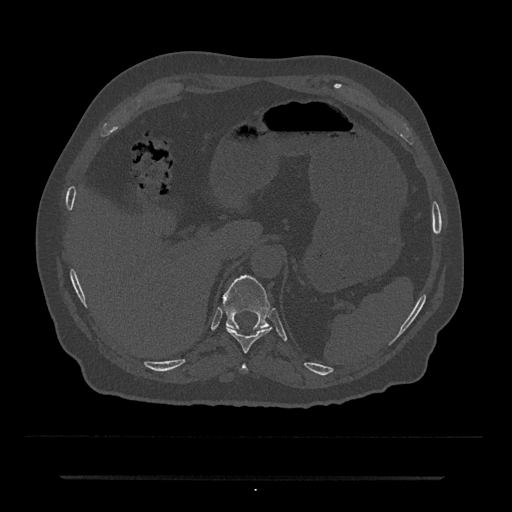
CT including the spine, one axial slice; slice 208 of 797 in the series (ordered by position); reconstruction kernel Br40s/3; bone window (W 1800 / L 400 HU); 512 × 512 image matrix, field of view 437 × 437 mm. Patient: male, 69 years. From the clinical record (not read from this slice): primary cancer: prostate.
Annotated regions visible in this slice (semi-automatically segmented with operator editing):
- T10 vertebra: bounding box <226,326,272,353> (left, top, right, bottom; pixels)
- T11 vertebra: <223,275,270,330>
- T9 vertebra: <241,364,248,371>